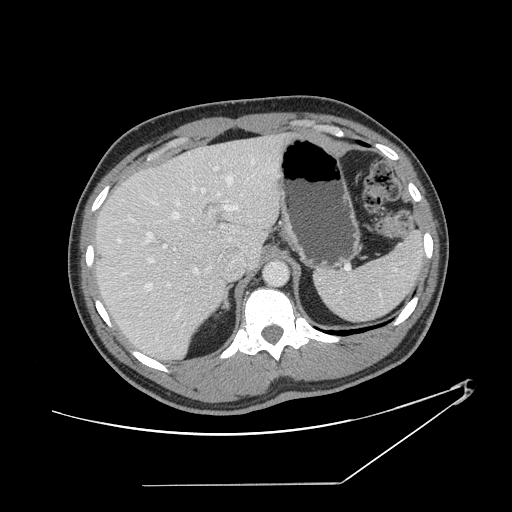
Contrast-enhanced abdominal CT, one axial slice; position 102 of 152 along the scan axis; soft-tissue window (W 400 / L 40 HU); 2.5 mm slice thickness; 512 × 512 image matrix. Male patient, age 45 years. From the clinical record (not read from this slice): diagnosis: colorectal cancer liver metastases, imaged before liver resection; multiple liver metastases: no.
Outlined on this slice (outlined manually by an expert reader):
- hepatic veins: bounding box [x1, y1, x2, y2] px = [111, 158, 255, 320]
- liver: [97, 135, 287, 358]
- planned liver remnant (the part of the liver to remain after resection): [97, 154, 232, 359]
- portal vein (with intrahepatic branches): [139, 167, 238, 341]